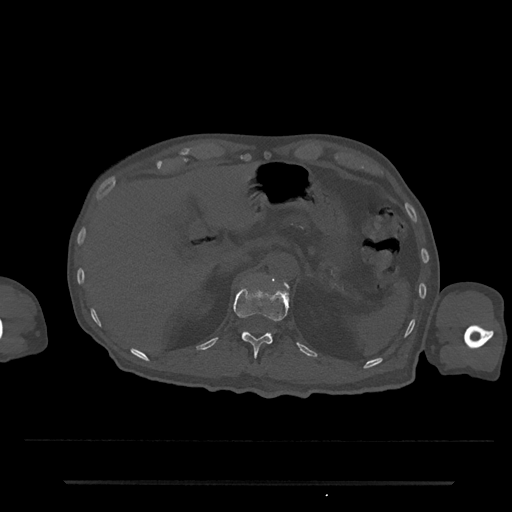
CT including the spine, one axial slice; slice 185 of 797 in the series (ordered by position); reconstruction kernel Br40s/3; 120 kVp; bone window (W 1800 / L 400 HU); 0.5 mm slice thickness; 512 × 512 image matrix, field of view 427 × 427 mm. Male patient, age 74 years. From the clinical record (not read from this slice): primary cancer: prostate.
Annotated regions visible in this slice (semi-automatically segmented with operator editing):
- T12 vertebra: bounding box (x1, y1, x2, y2) in pixels: (234, 286, 289, 357)